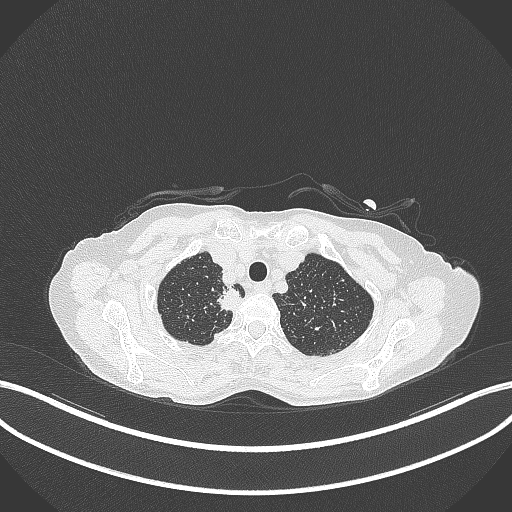
Chest CT, one axial slice. Position 326 of 403 along the scan axis. Lung window (W 1500 / L -600 HU). 1 mm slice thickness. 512 × 512 image matrix, field of view 400 × 400 mm. Patient: female, 75 years. Case-level facts recorded for this patient, not image findings: clinical TNM (as recorded): T1c N1 M1.
Structures marked on this image (rectangle marked by the reading radiologist):
- lung tumour (recorded histology: adenocarcinoma): bounding box <214,283,244,314> (left, top, right, bottom; pixels)